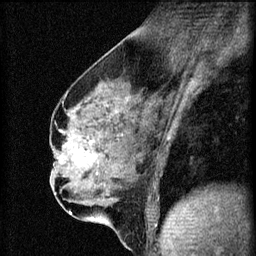
Breast MRI (dynamic contrast-enhanced), one sagittal slice; slice 33 of 60 in the series (ordered by position); 3 images stored at this slice position (order not interpretable as contrast timing); 1.5 T; TE 4.2 ms, TR 8.2 ms; 256 × 256 image matrix, field of view 180 × 180 mm. Patient: female, 56 years.
Annotated regions visible in this slice (semi-automatically segmented with operator editing):
- analysis volume of interest (the breast-tissue region the enhancement analysis was run in; not a lesion): bounding box <62,136,111,179> (left, top, right, bottom; pixels)
- tumour enhancement mask (voxels above the 70 % enhancement threshold inside the analysis volume of interest): <62,138,98,175>